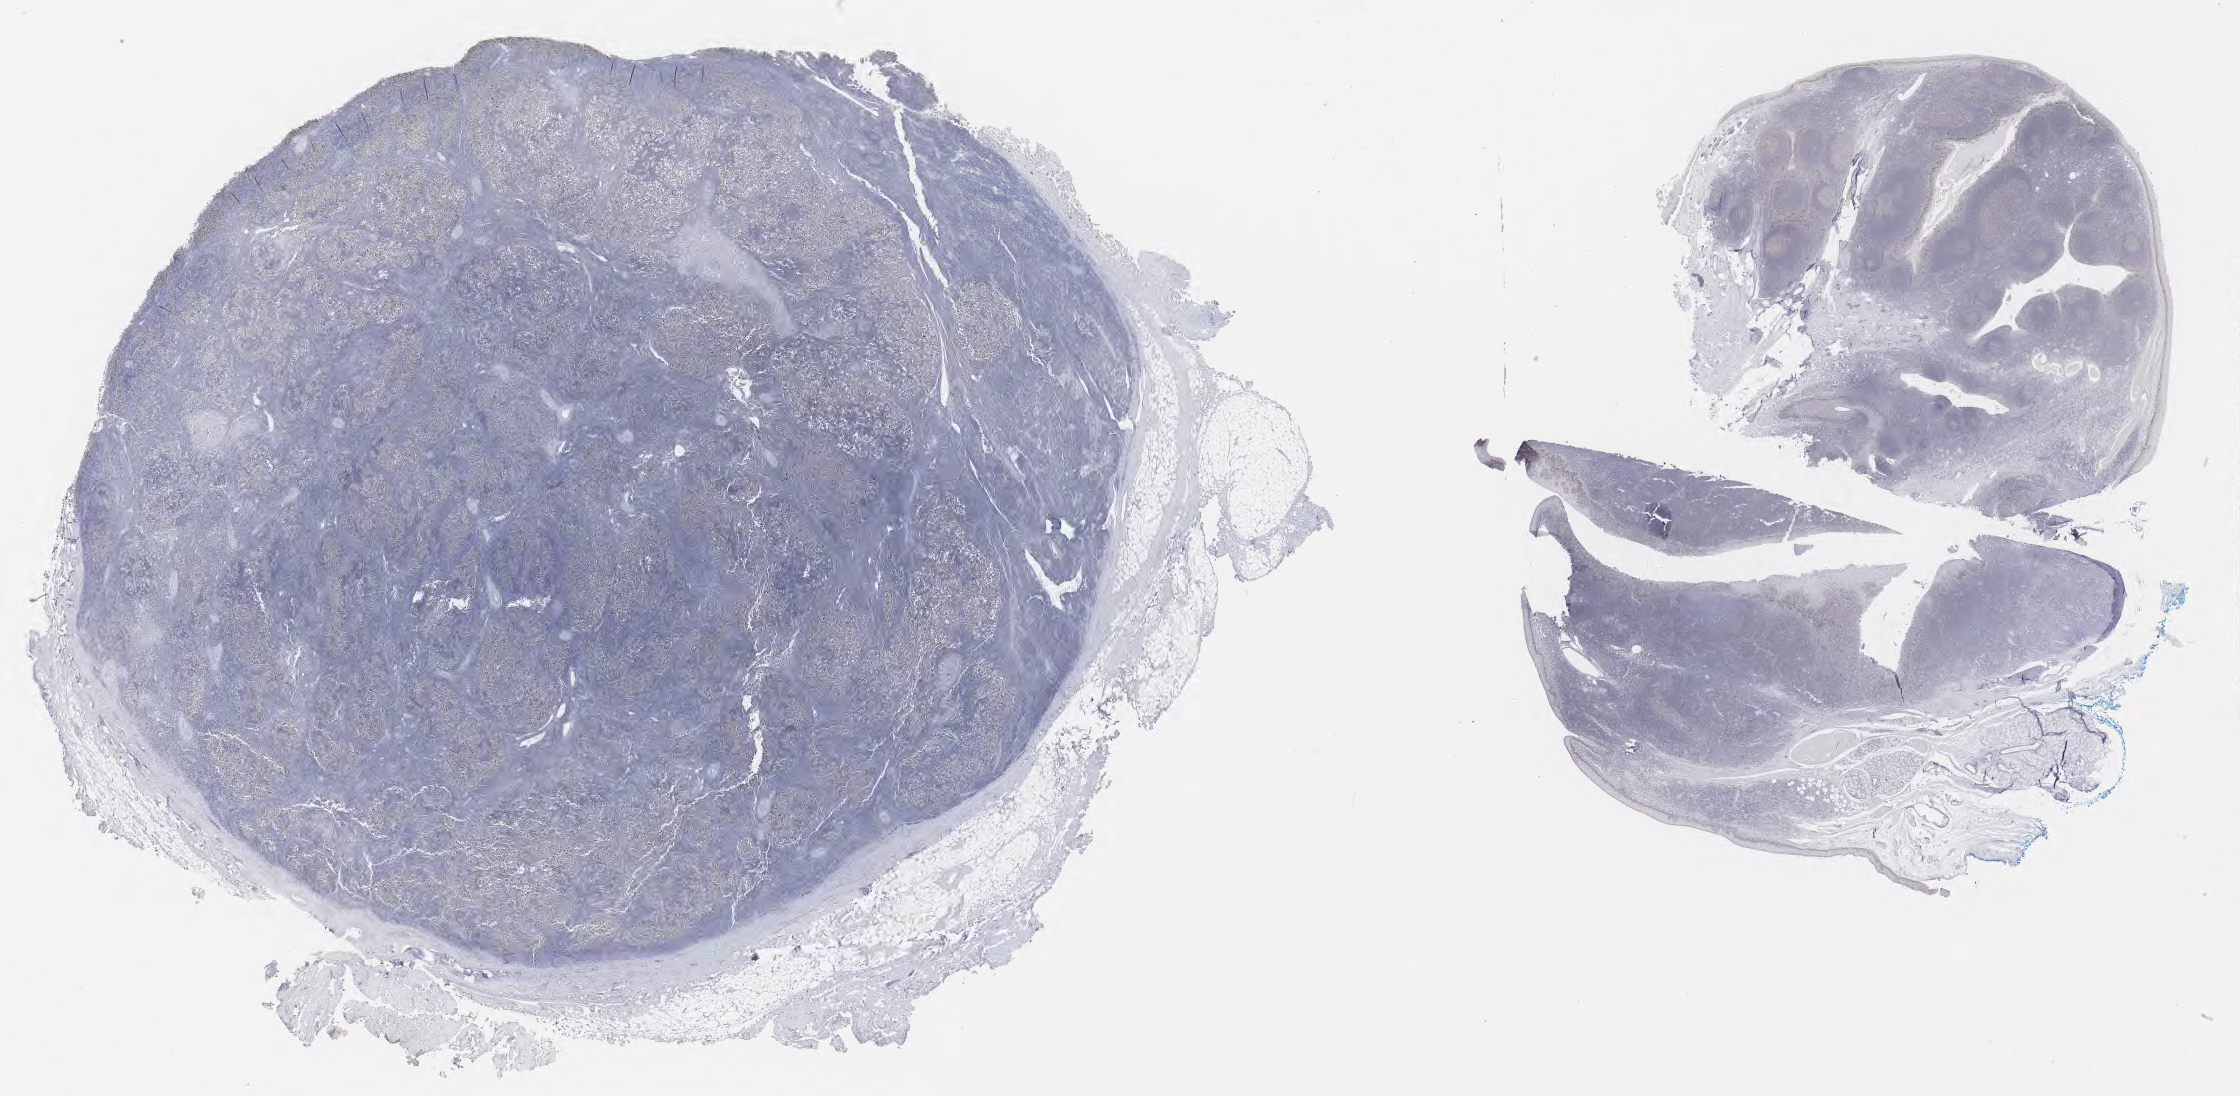
Whole-slide image, immunohistochemical stain for p53, whole scanned area (about 36.2 x 17.7 mm) shown as a low-resolution overview, tumor tissue, site: lymph node. Male patient, 46 years old.
Histologic diagnosis: Diffuse large B-cell lymphoma, NOS.